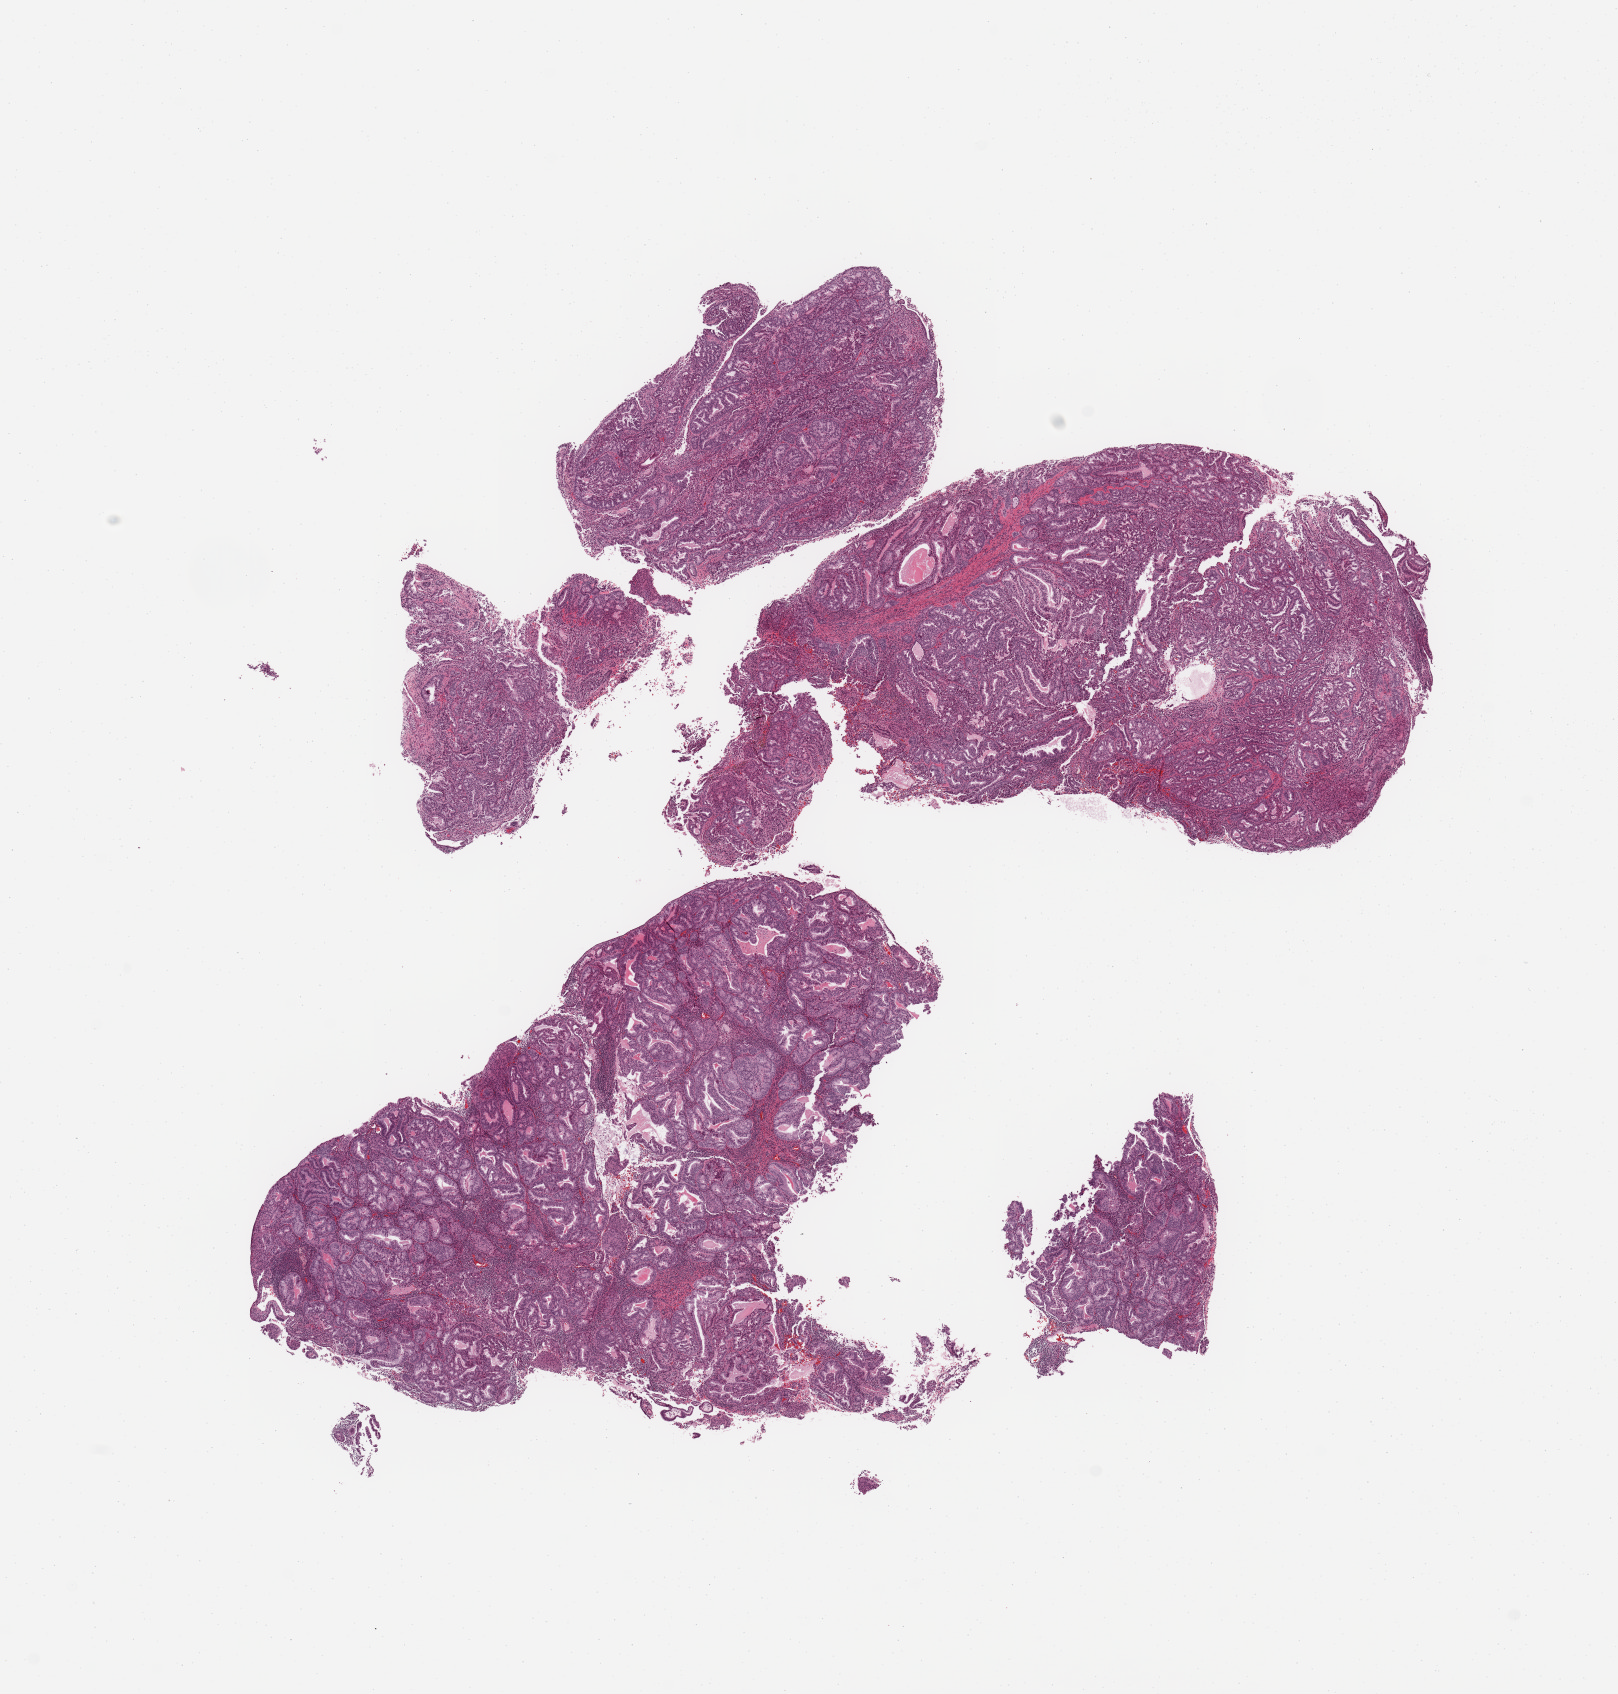
H&E whole-slide image — shown as a low-resolution overview of the whole scanned area (about 12.8 x 13.4 mm, slide scanned at 20x), tumour tissue sample, uterus. Female, 68 y/o. Histologic grade: G1 (well differentiated).
- AJCC pathologic stage: I
- histologic diagnosis: Endometrioid adenocarcinoma, NOS